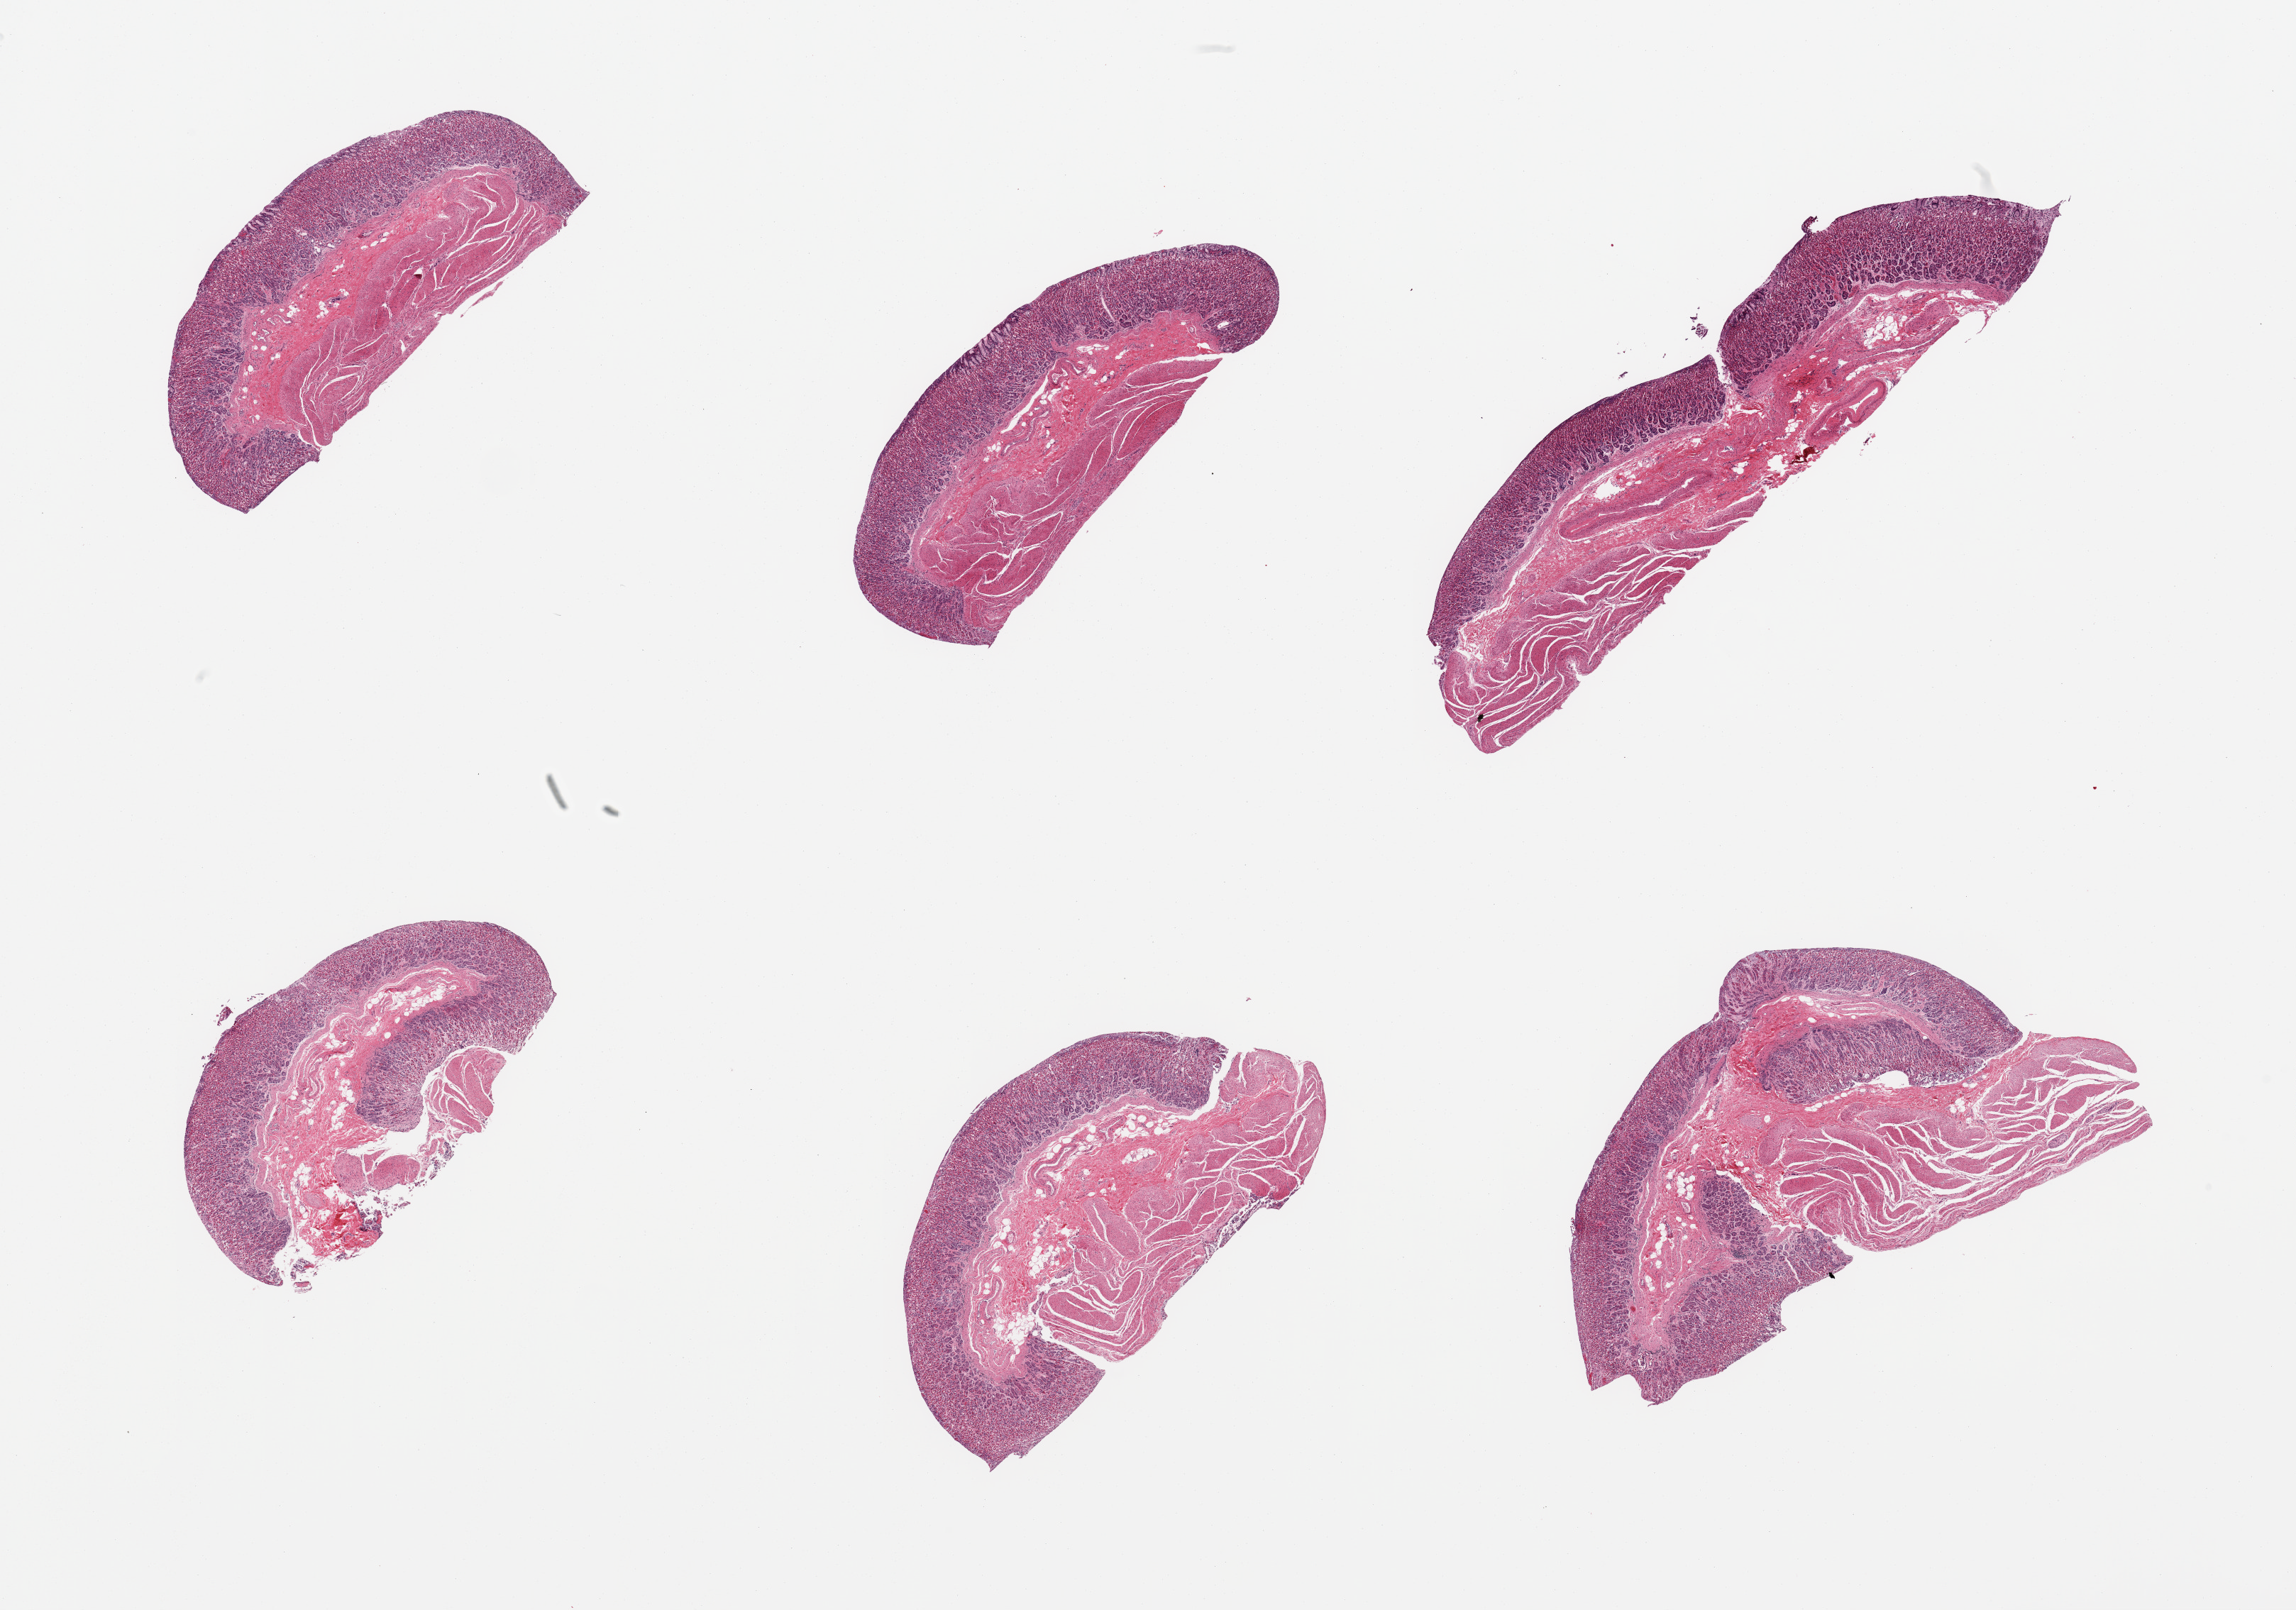
Whole-slide image, hematoxylin and eosin (H&E) stain, brightfield — low-resolution overview of the scanned area, about 25.6 x 17.9 mm, PAXgene-fixed, paraffin-embedded tissue, target tissue: stomach, donor tissue sample. Donor: male.
Review note (as recorded): 6 pieces.